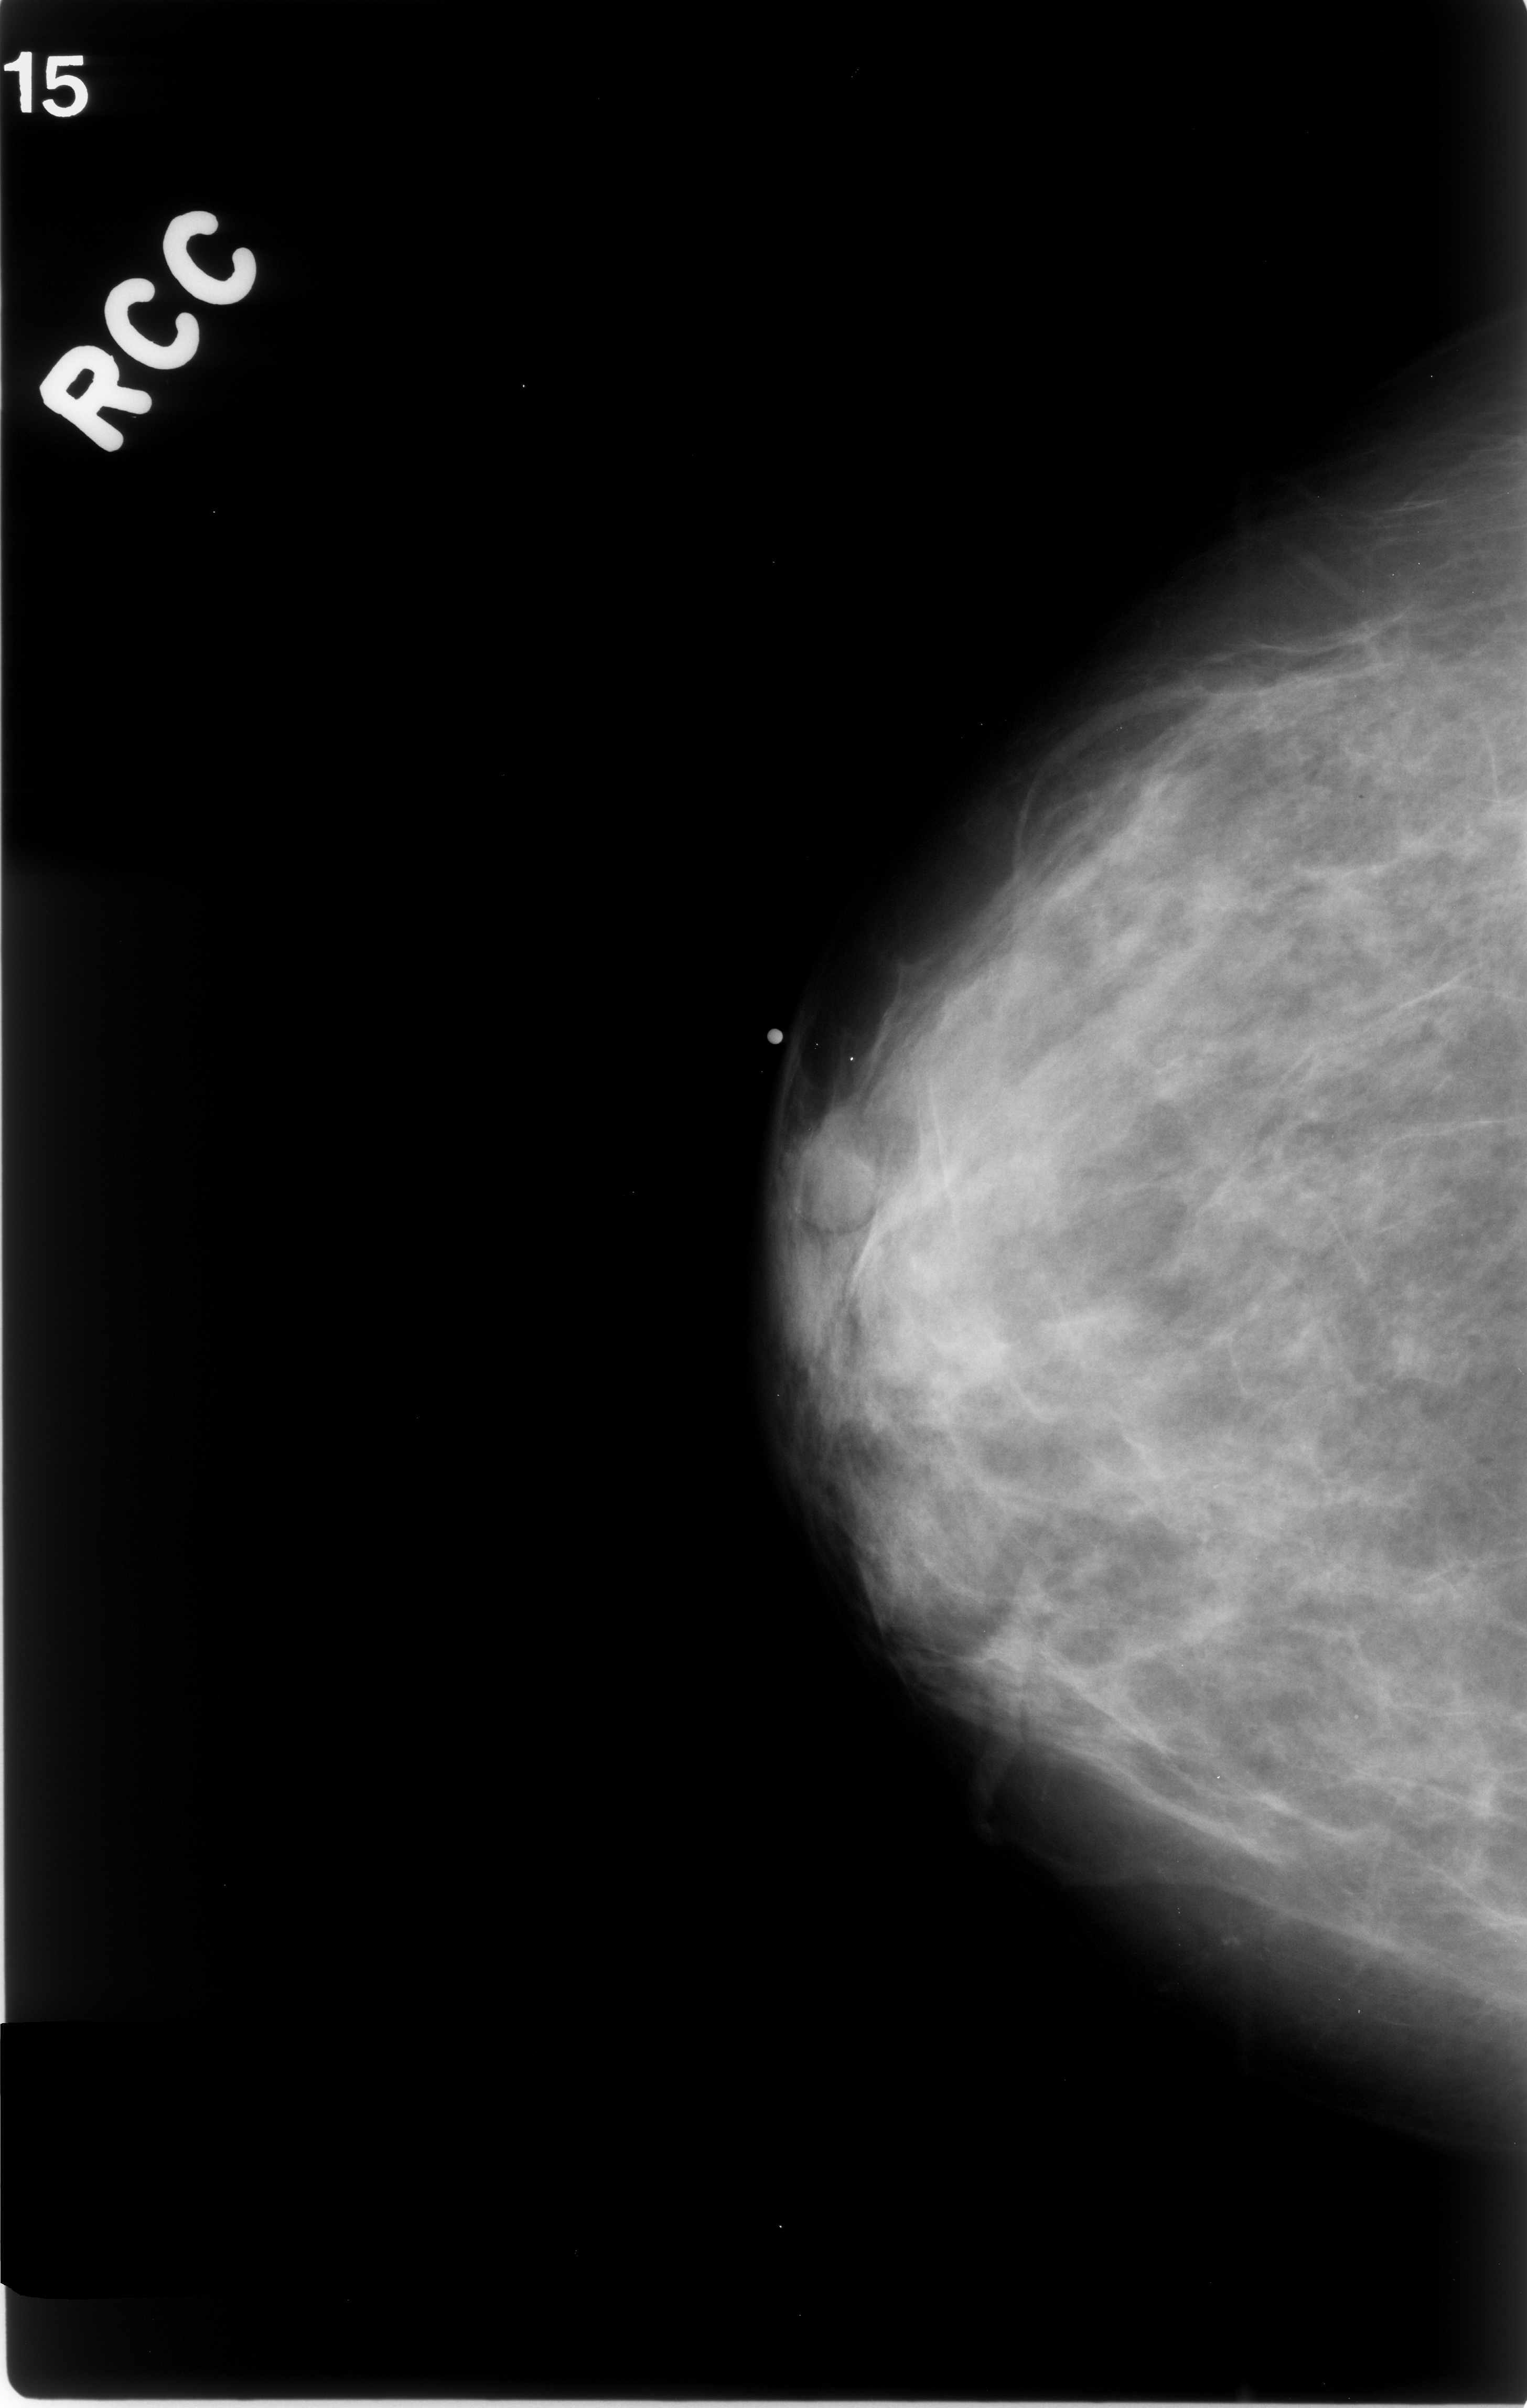
Mammogram (digitized film). Right breast. CC view. 1527 × 2408 image matrix.
Expert-marked regions of interest on this film, with their recorded descriptors:
- mass, shape round, margins circumscribed; BI-RADS assessment category 3; subtlety rating 5 on a 1 (subtle) to 5 (obvious) scale; pathology (as recorded): benign: bounding box (x1, y1, x2, y2) in pixels: (782, 1111, 876, 1225)